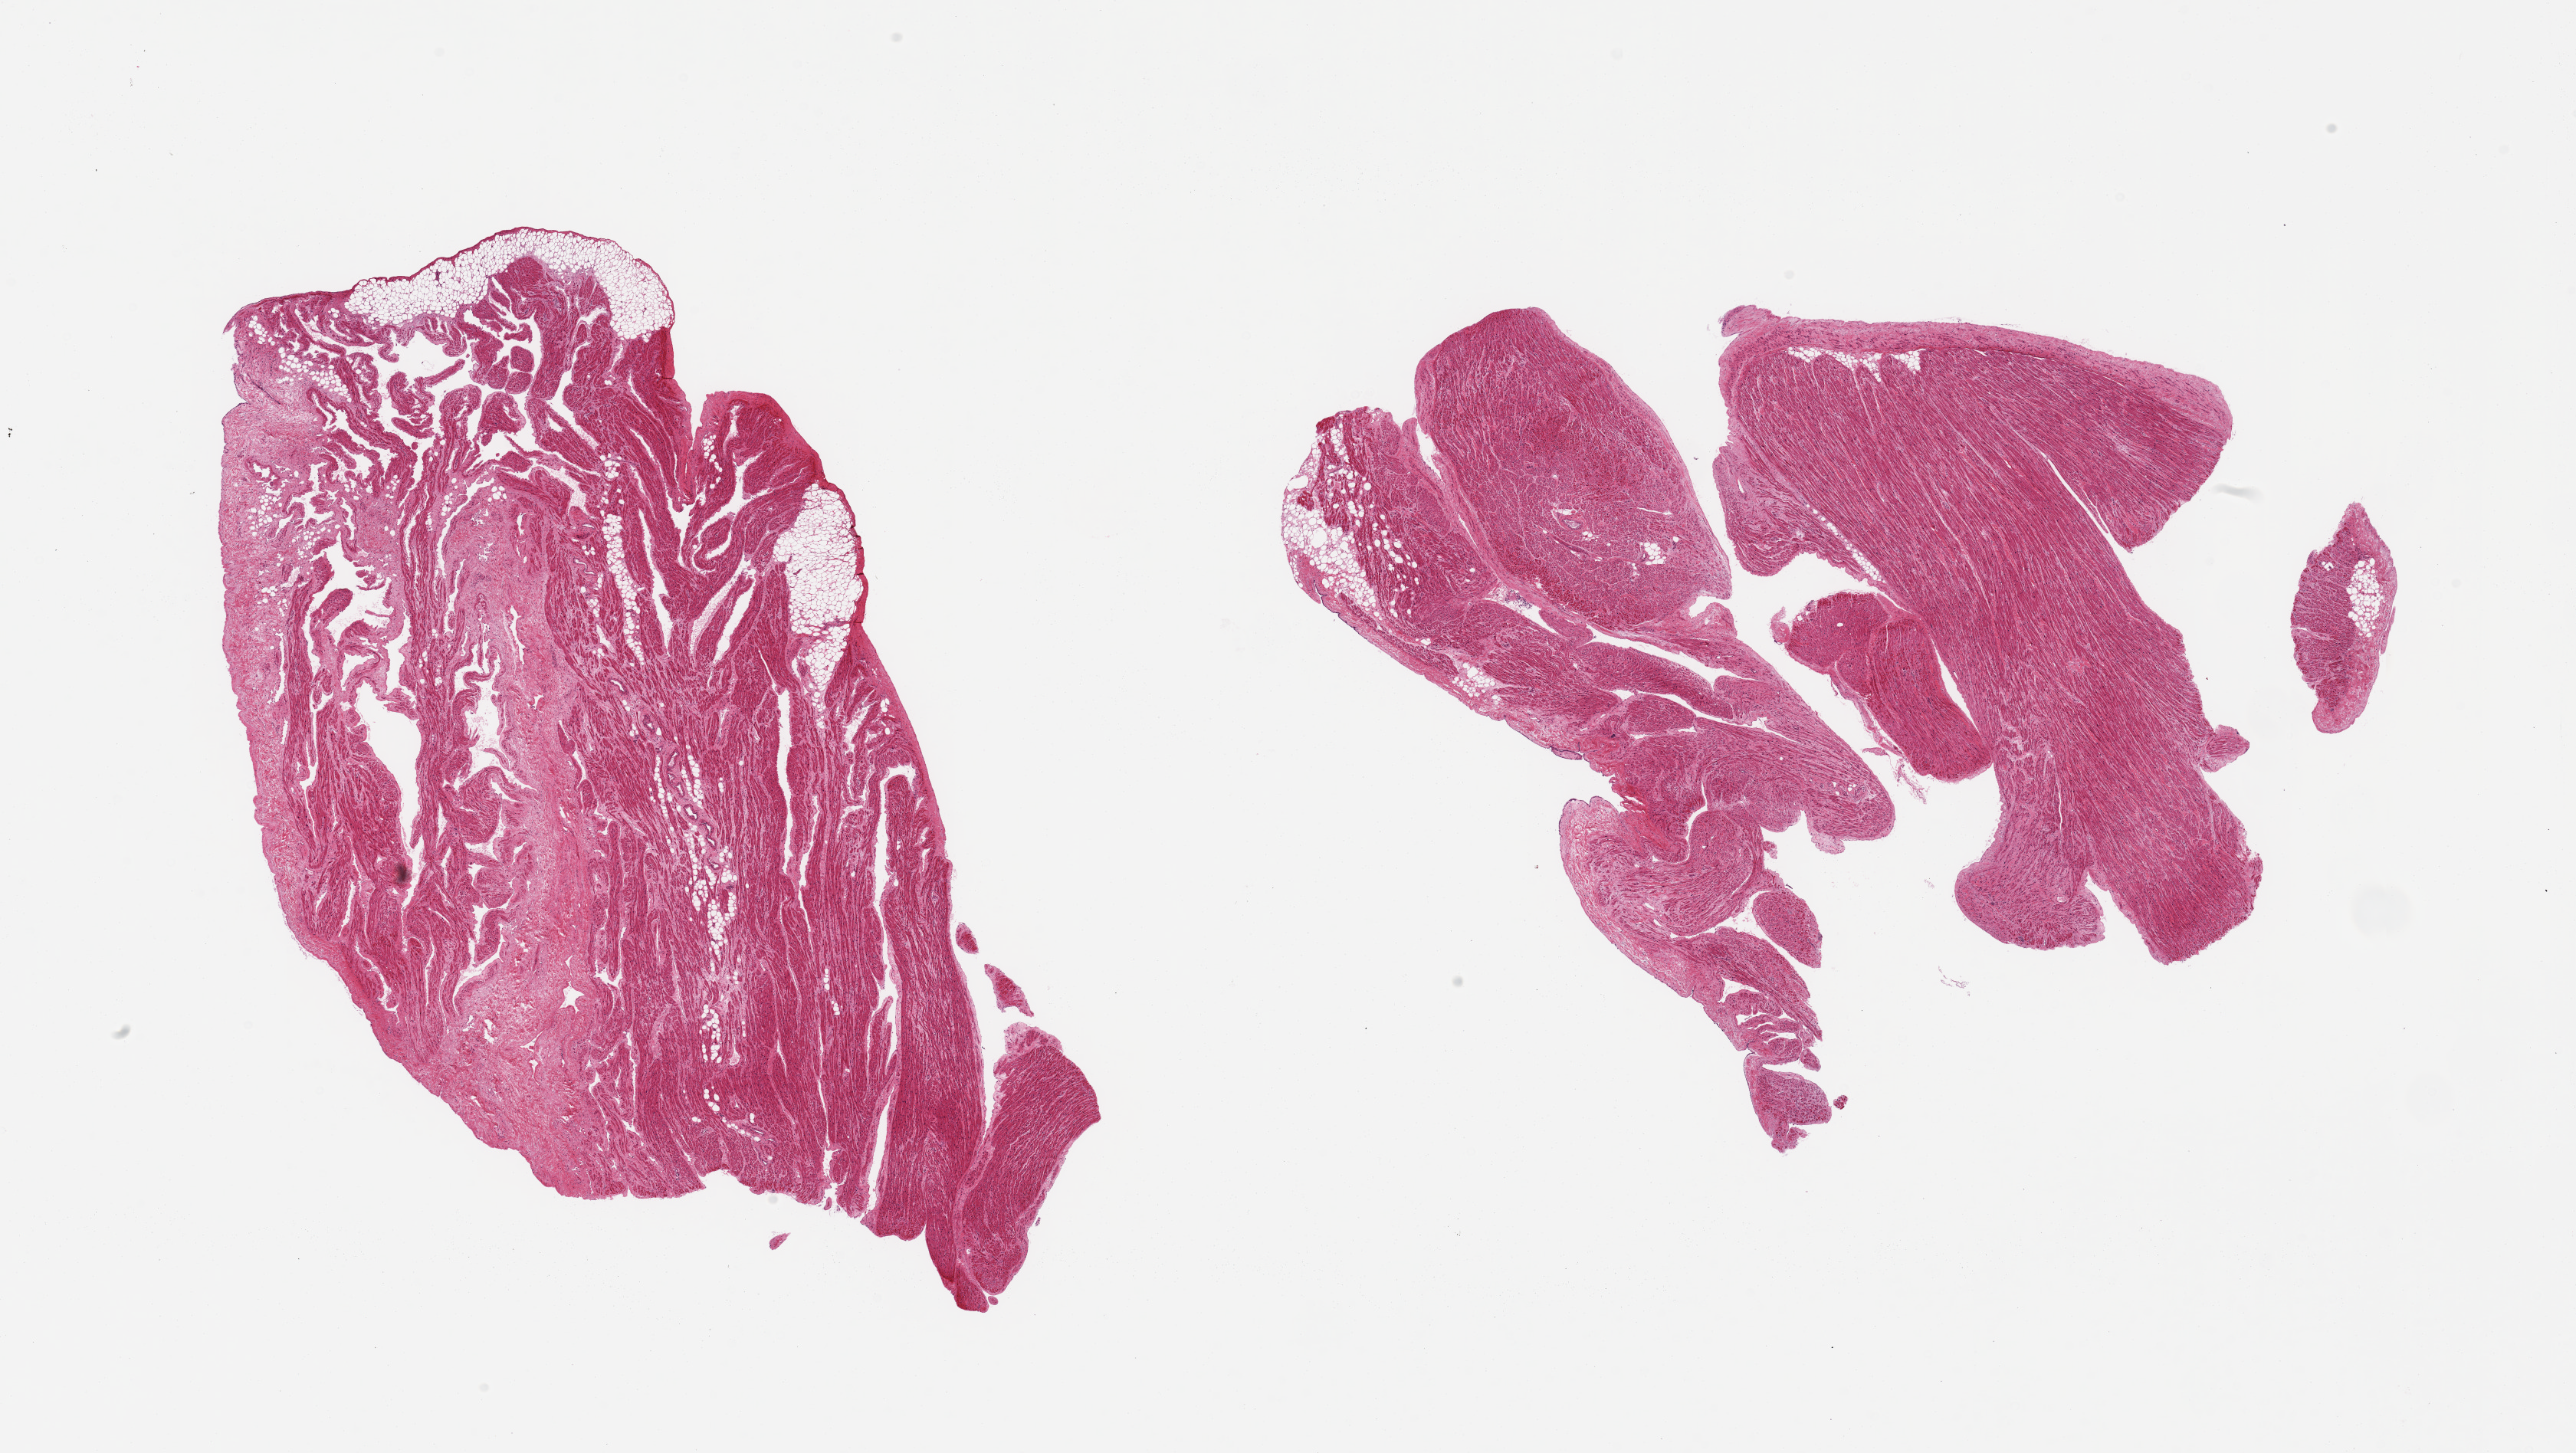
H&E whole-slide image, whole scanned area (about 26.6 x 15.0 mm, from a 20x scan) shown as a low-resolution overview, PAXgene-fixed, paraffin-embedded tissue, sampled site (target tissue): auricular appendage, donor tissue sample. Donor: male.
Pathologist's review note for this sample: 2 pieces, no abnormalities.